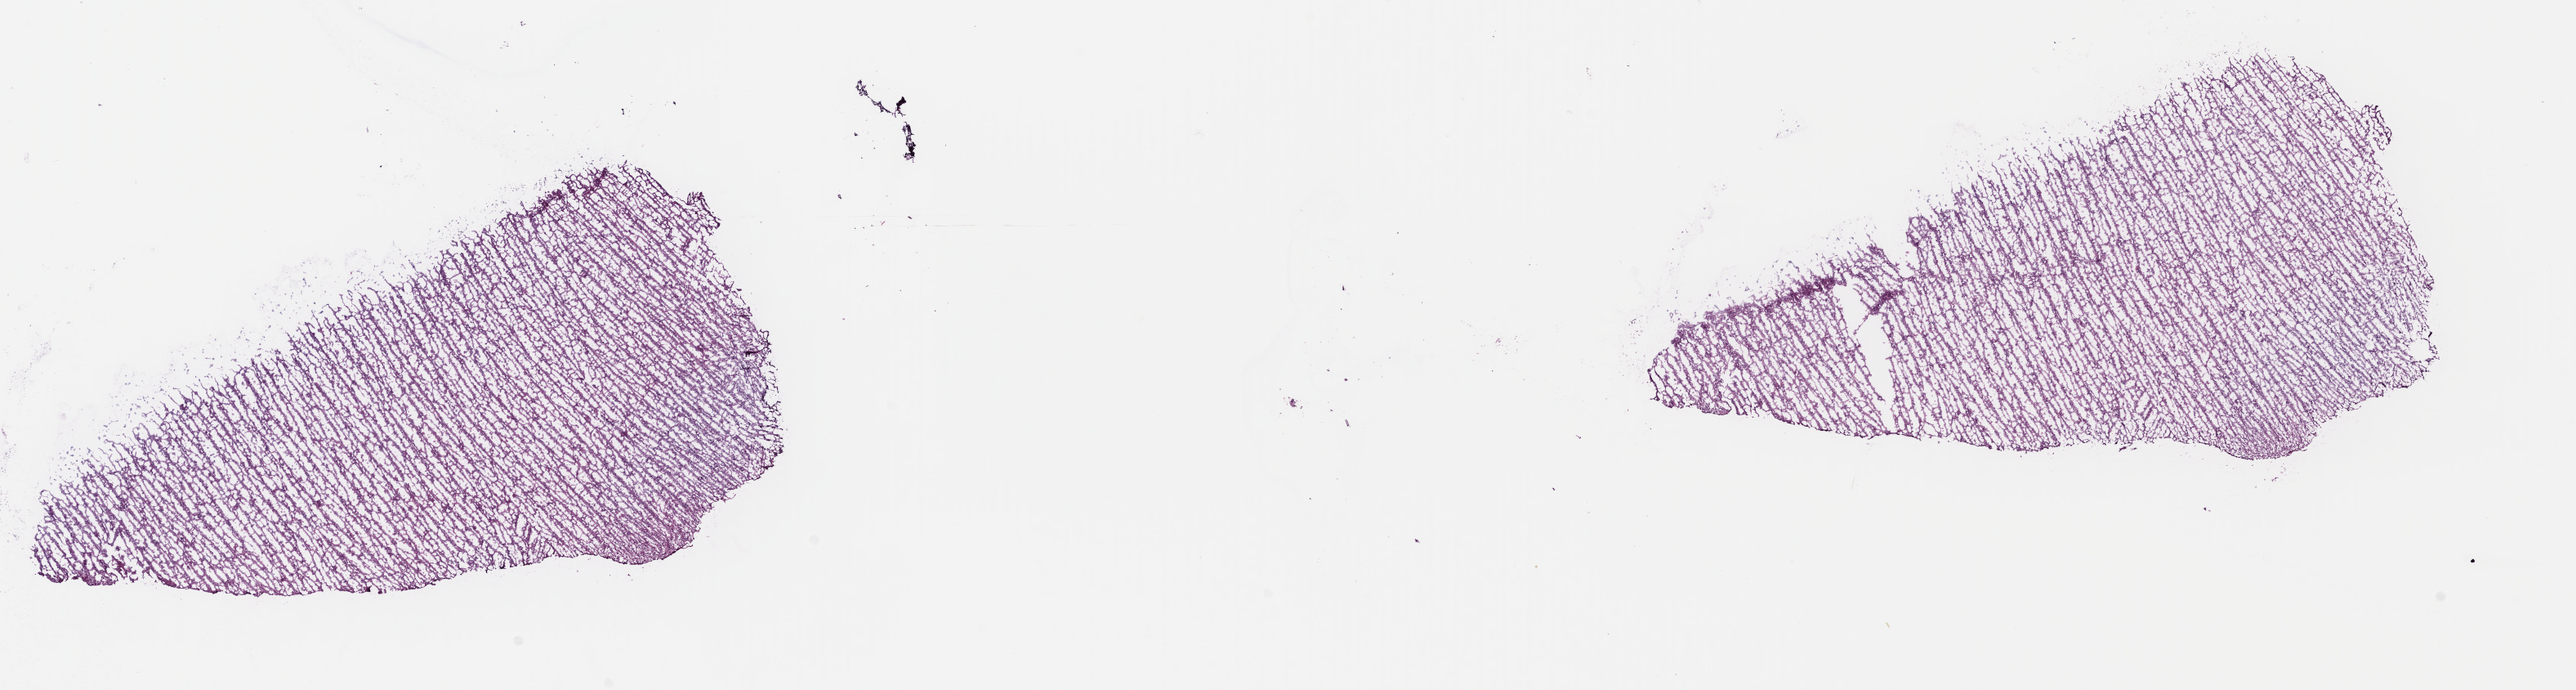
Whole-slide histology image, Hematoxylin and eosin (H&E) stained, whole scanned area (about 24.8 x 6.6 mm) shown as a low-resolution overview; frozen section from the top of the tissue portion; brain, primary tumour sample. Female, age 38 years at initial diagnosis. Histologic grade: G2 (moderately differentiated). Pathologist review of this section (percent, as recorded): tumour cells 60%, tumour nuclei 80%, normal cells 5%, stromal cells 35%, necrosis 0%. Infiltration values recorded for this section: lymphocyte infiltration 0%, monocyte infiltration 0%, neutrophil infiltration 0%.
Laterality: left. Pathologic diagnosis: Astrocytoma, NOS.